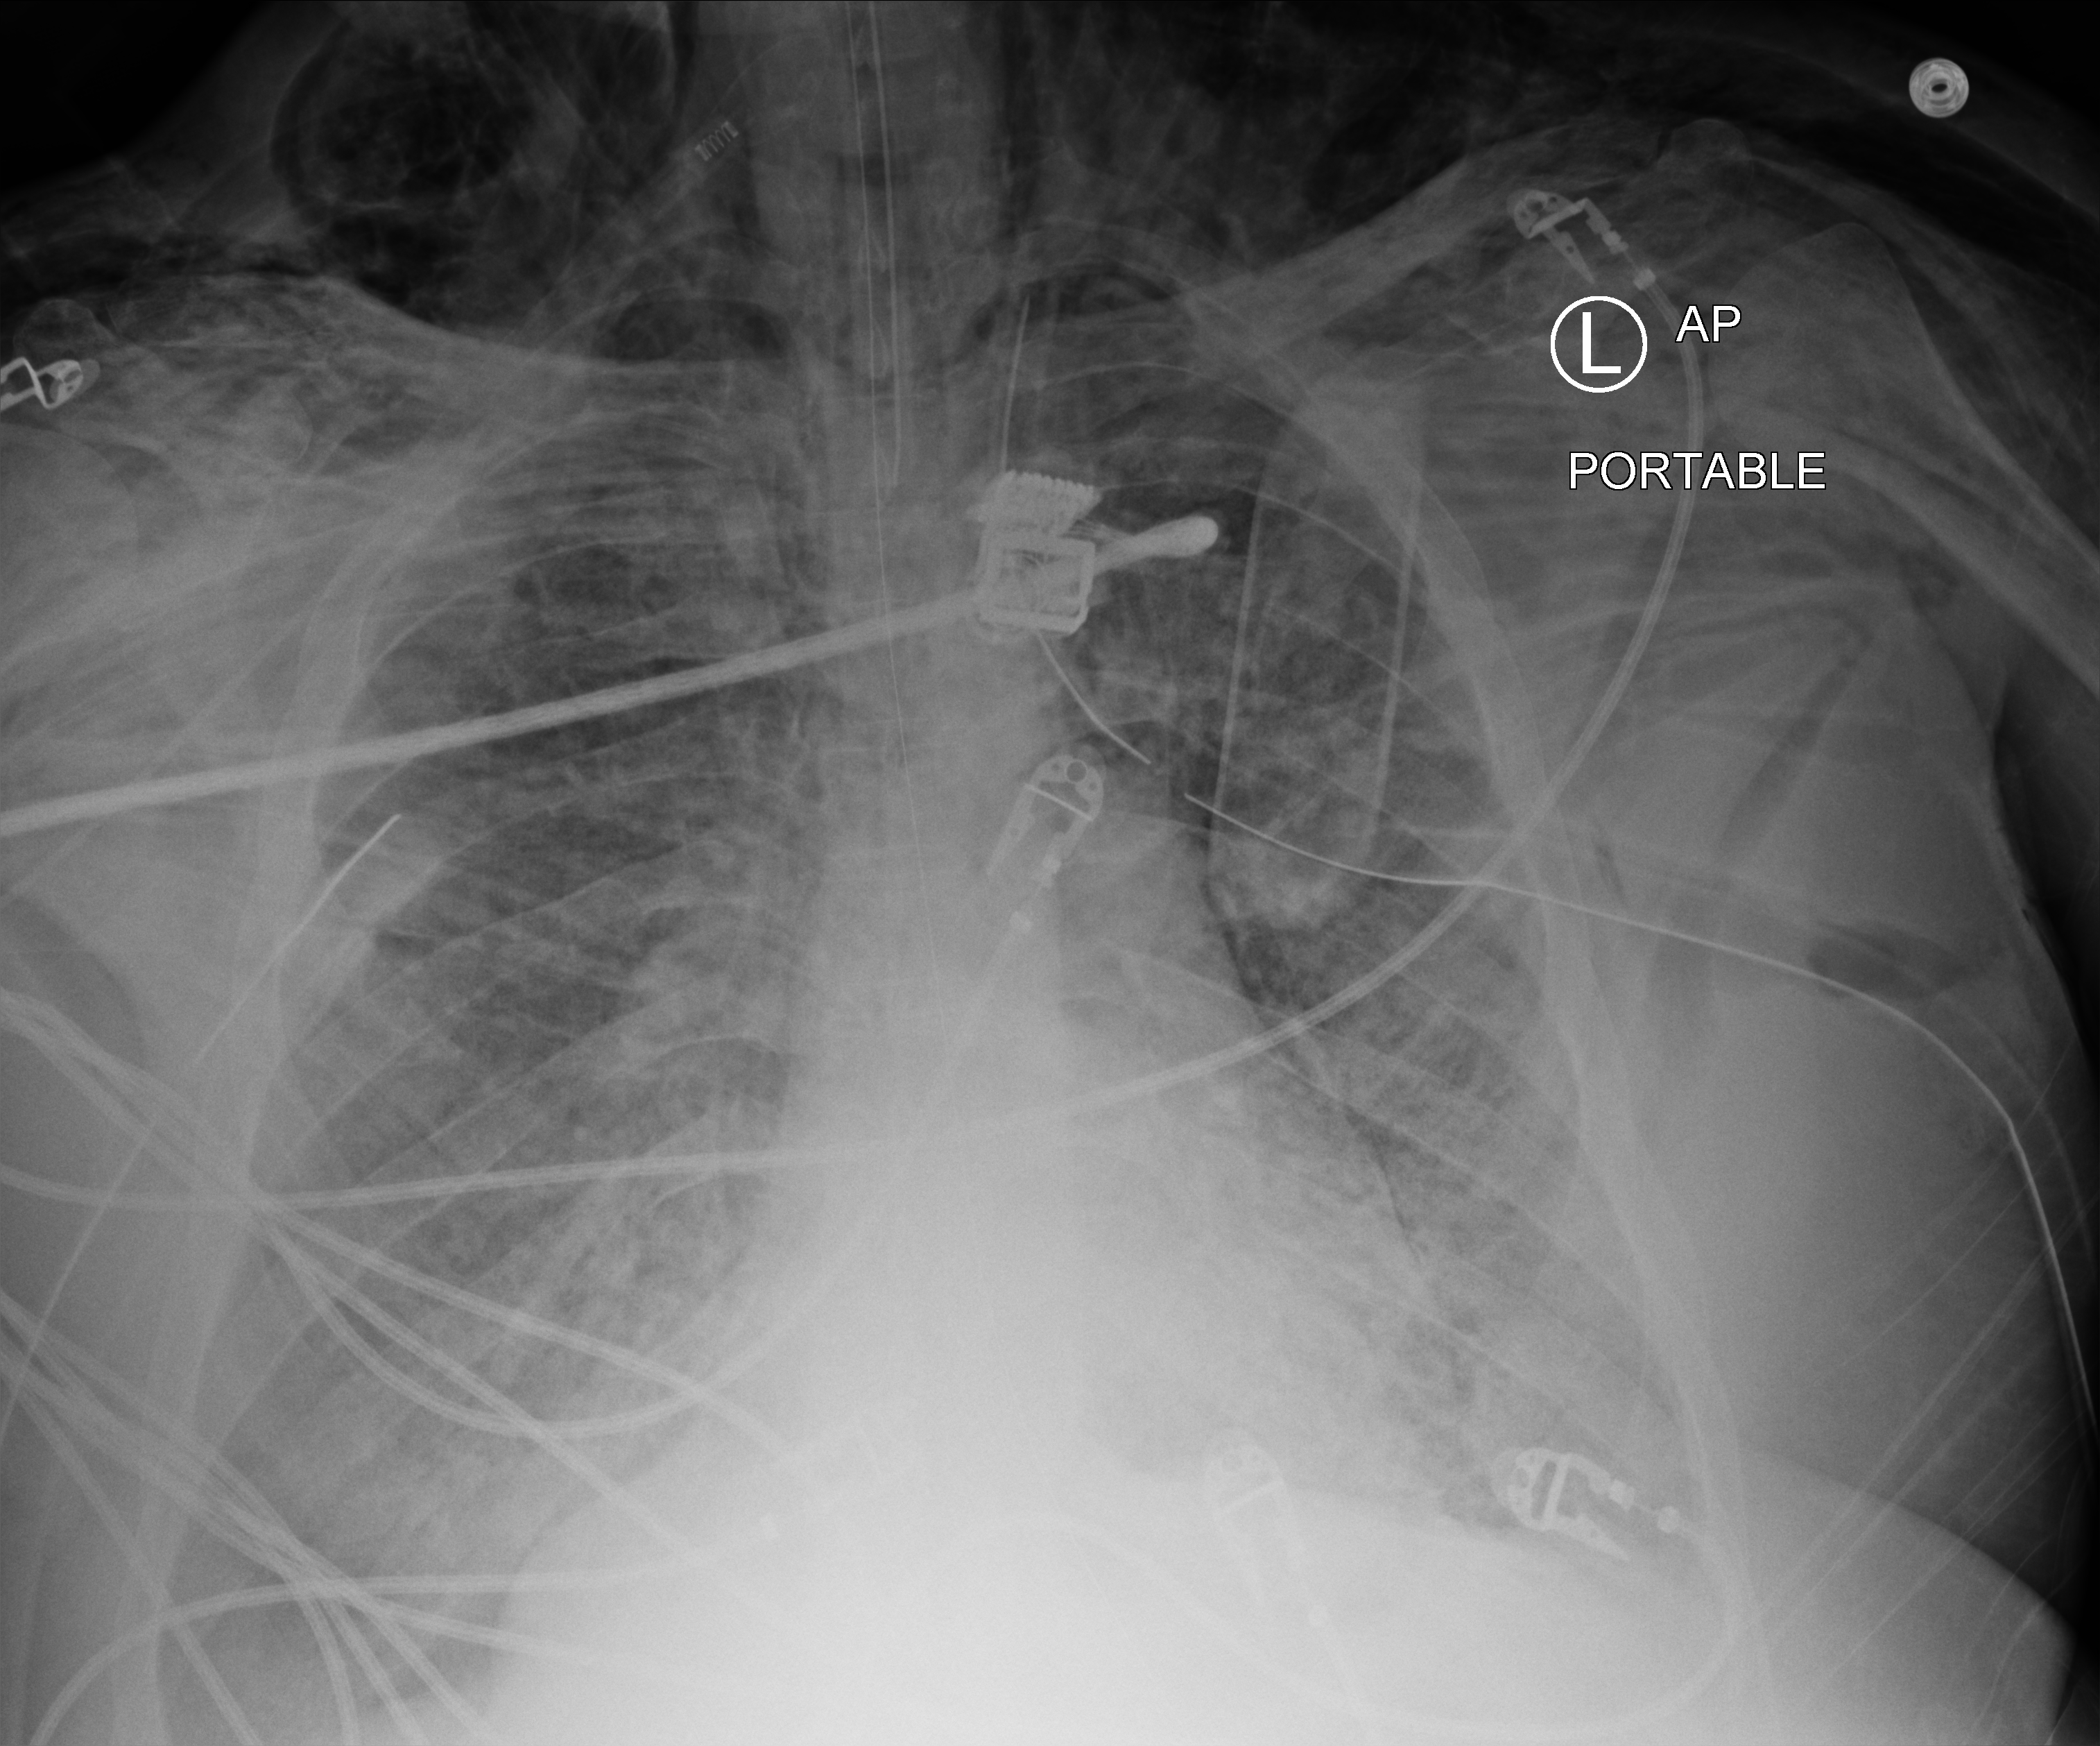
Portable chest radiograph, anteroposterior (AP) projection. Adult patient hospitalised with COVID-19, age 18–59 years.
Hospital-stay facts (about this admission, not read from this image; timing relative to this image not recorded):
- admitted to intensive care during this hospital stay: yes